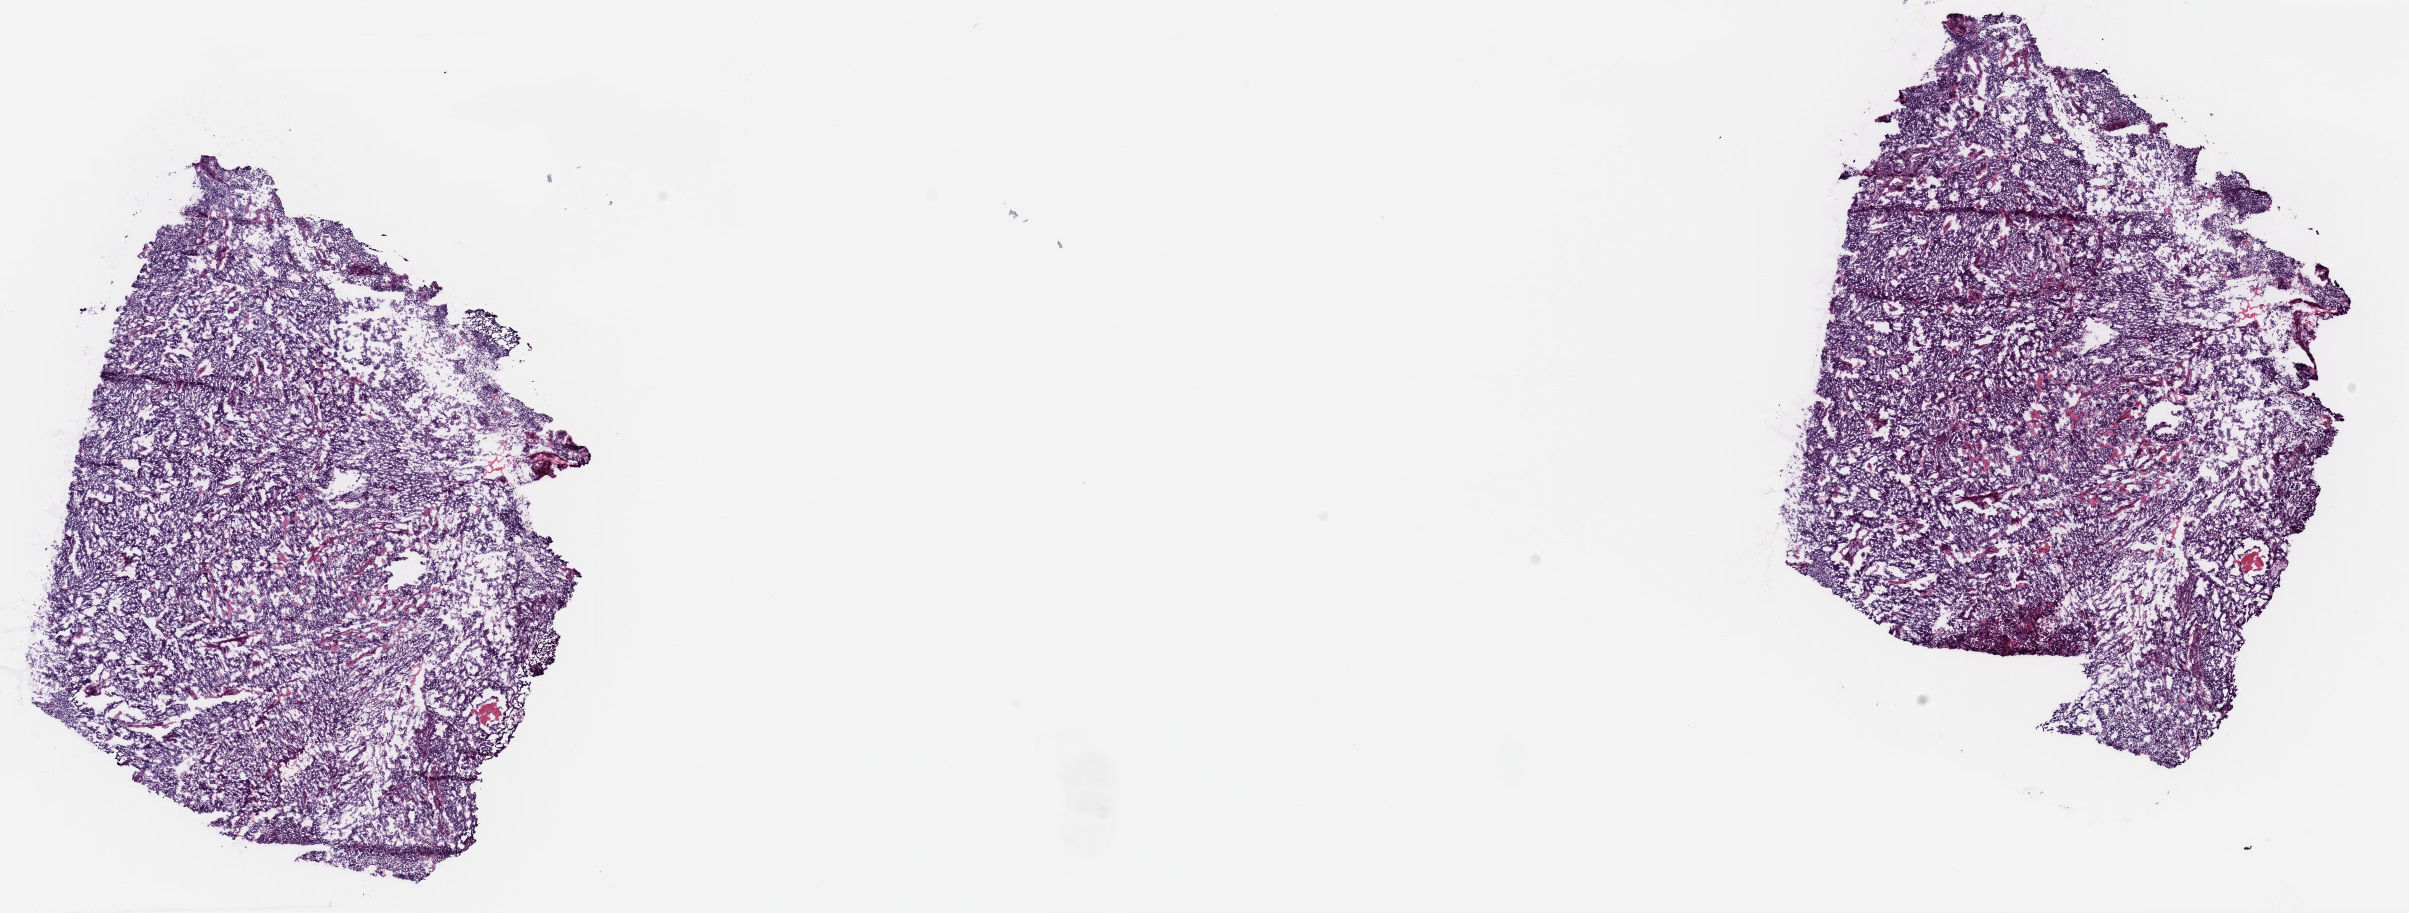
Whole-slide histology image, H&E-stained, a low-resolution overview of the entire scanned area, about 19.0 x 7.2 mm (acquisition: 40x scan). Frozen section. Uterus, primary tumour sample. Female patient. Composition of this section per pathologist review: tumour cells 93%, tumour nuclei 97%.
Histologic diagnosis: Endometrioid adenocarcinoma, NOS (endometrium).